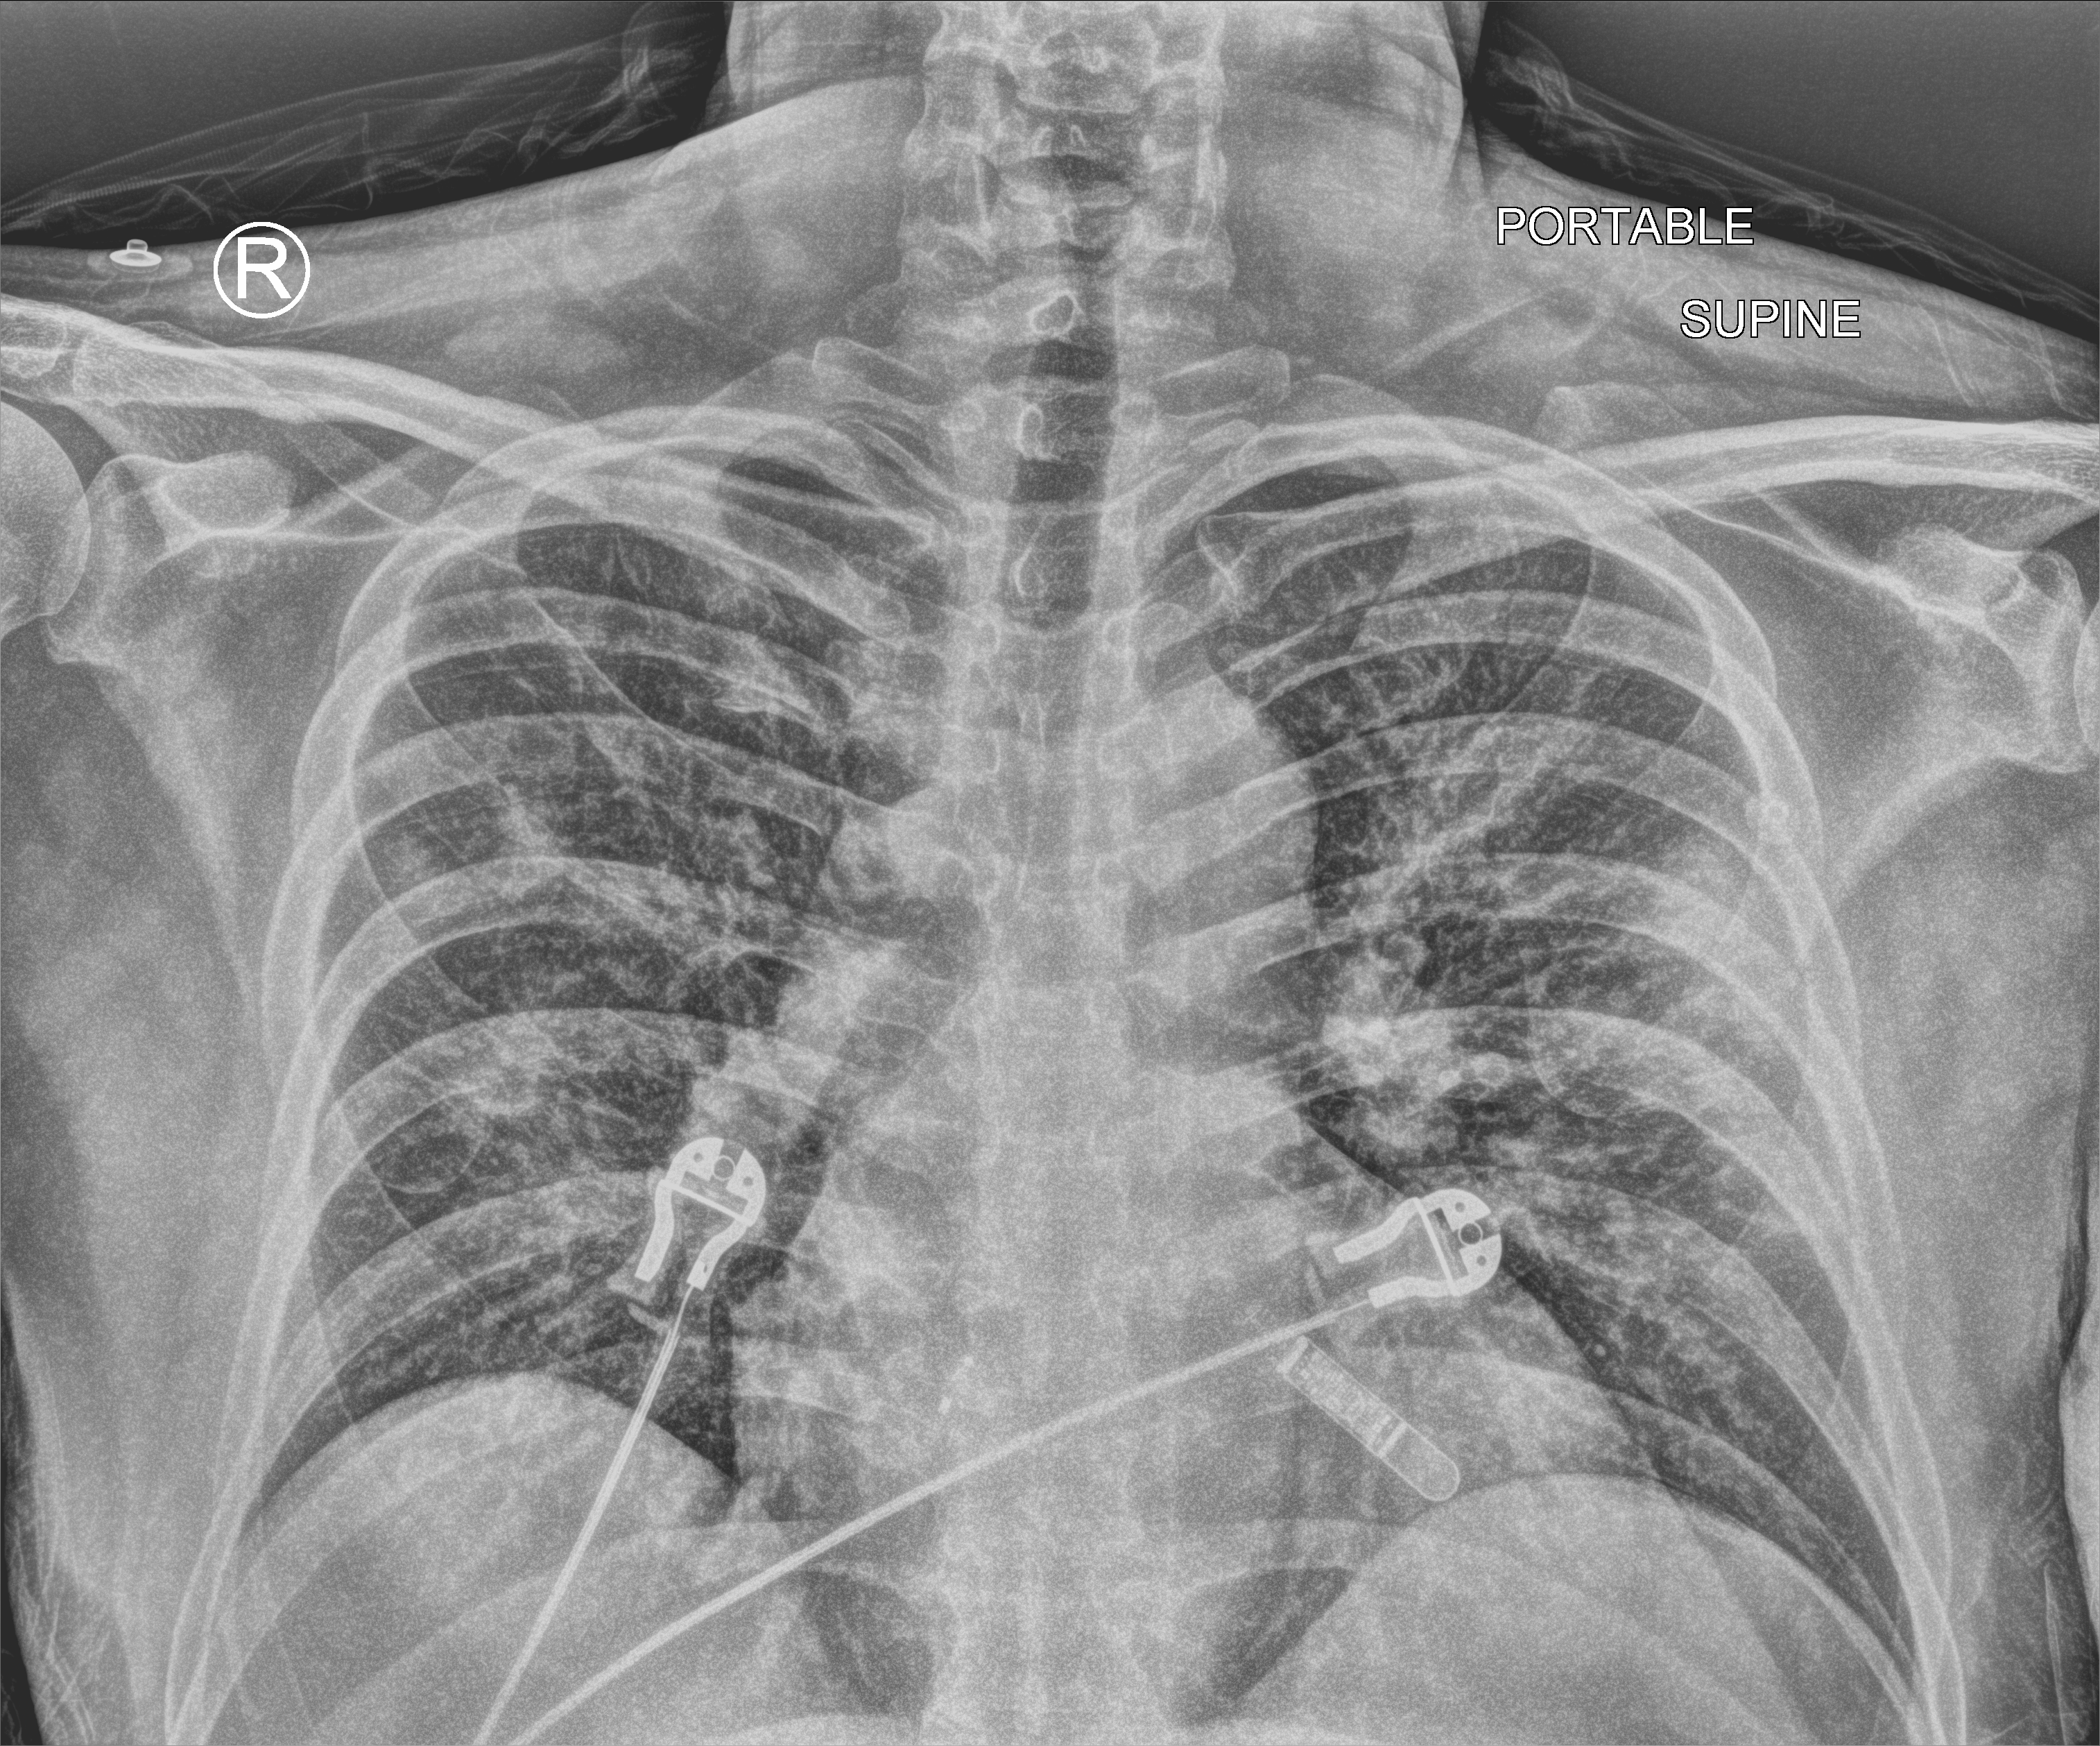
Bedside chest radiograph (computed radiography); anteroposterior (AP) projection. Patient hospitalised with COVID-19; male, aged 18–59 years.
From the hospital-stay record, not from the radiograph (when in the stay this image was taken is not recorded): diabetes (admission record): no.